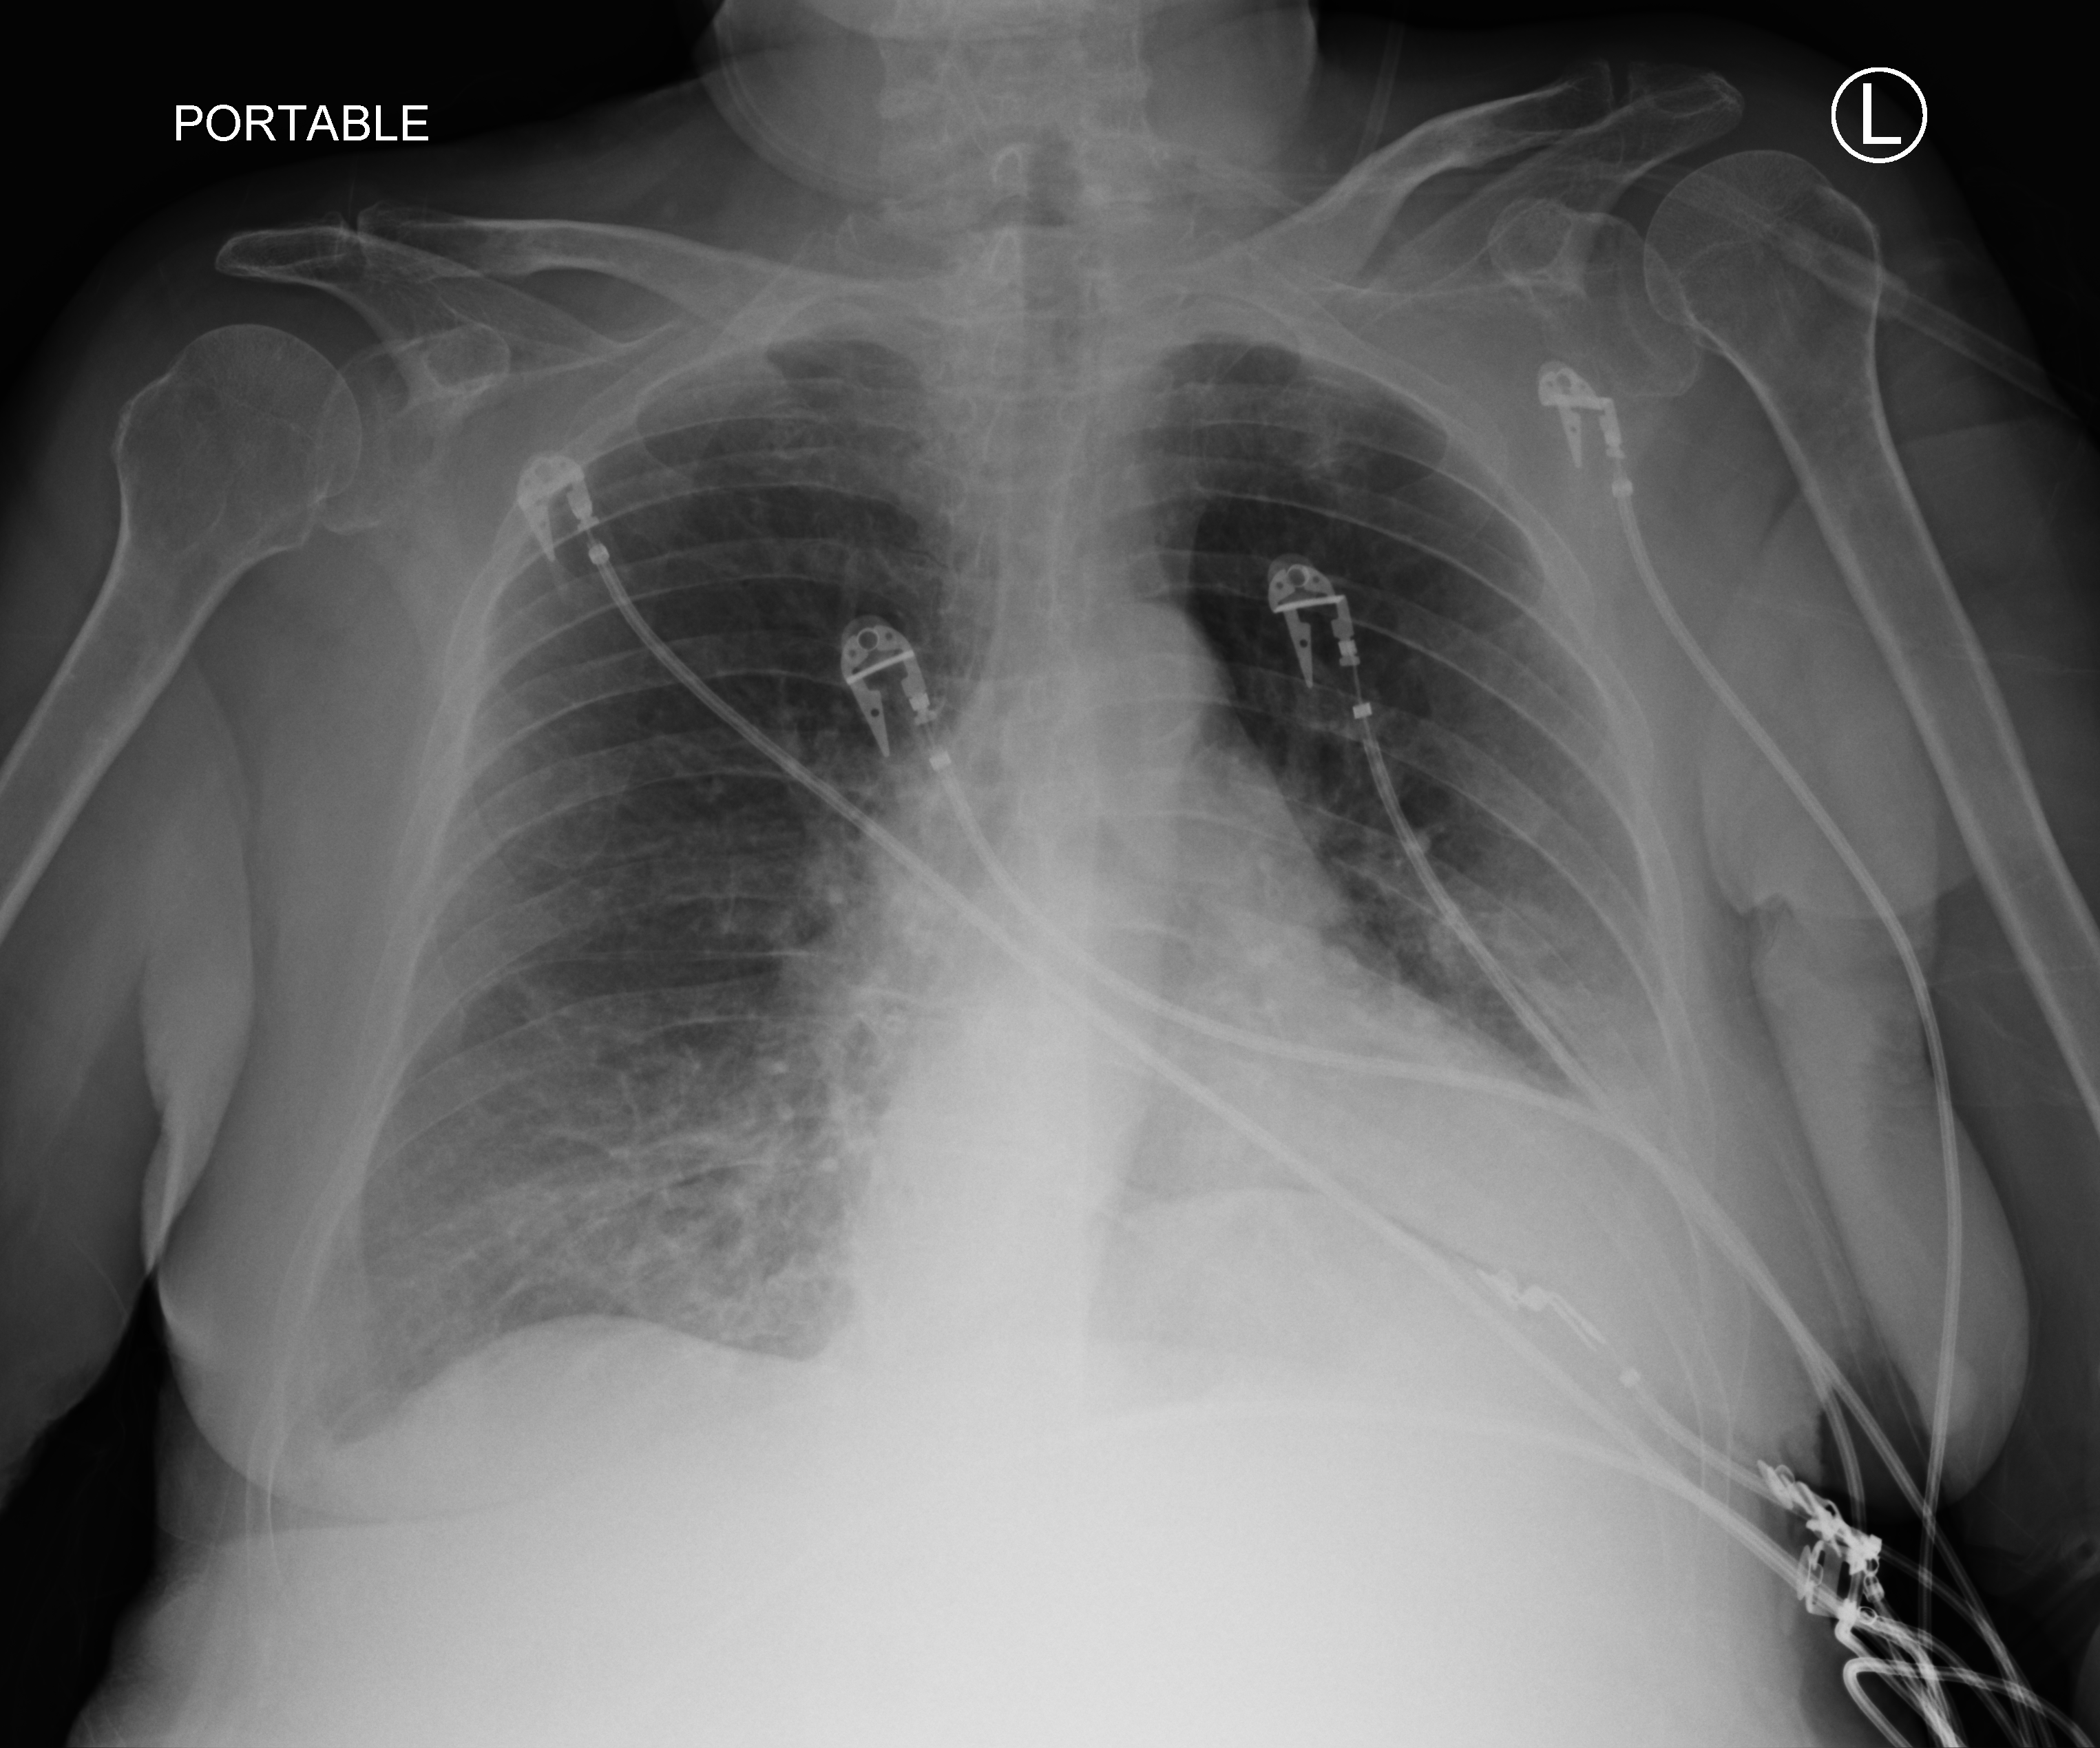
Bedside chest radiograph (computed radiography); anteroposterior (AP) projection. Female patient hospitalised with COVID-19, age 75–90 years.
Admission-level facts for this patient (not findings on this image; timing relative to this image not recorded):
- admitted to intensive care during this hospital stay: no